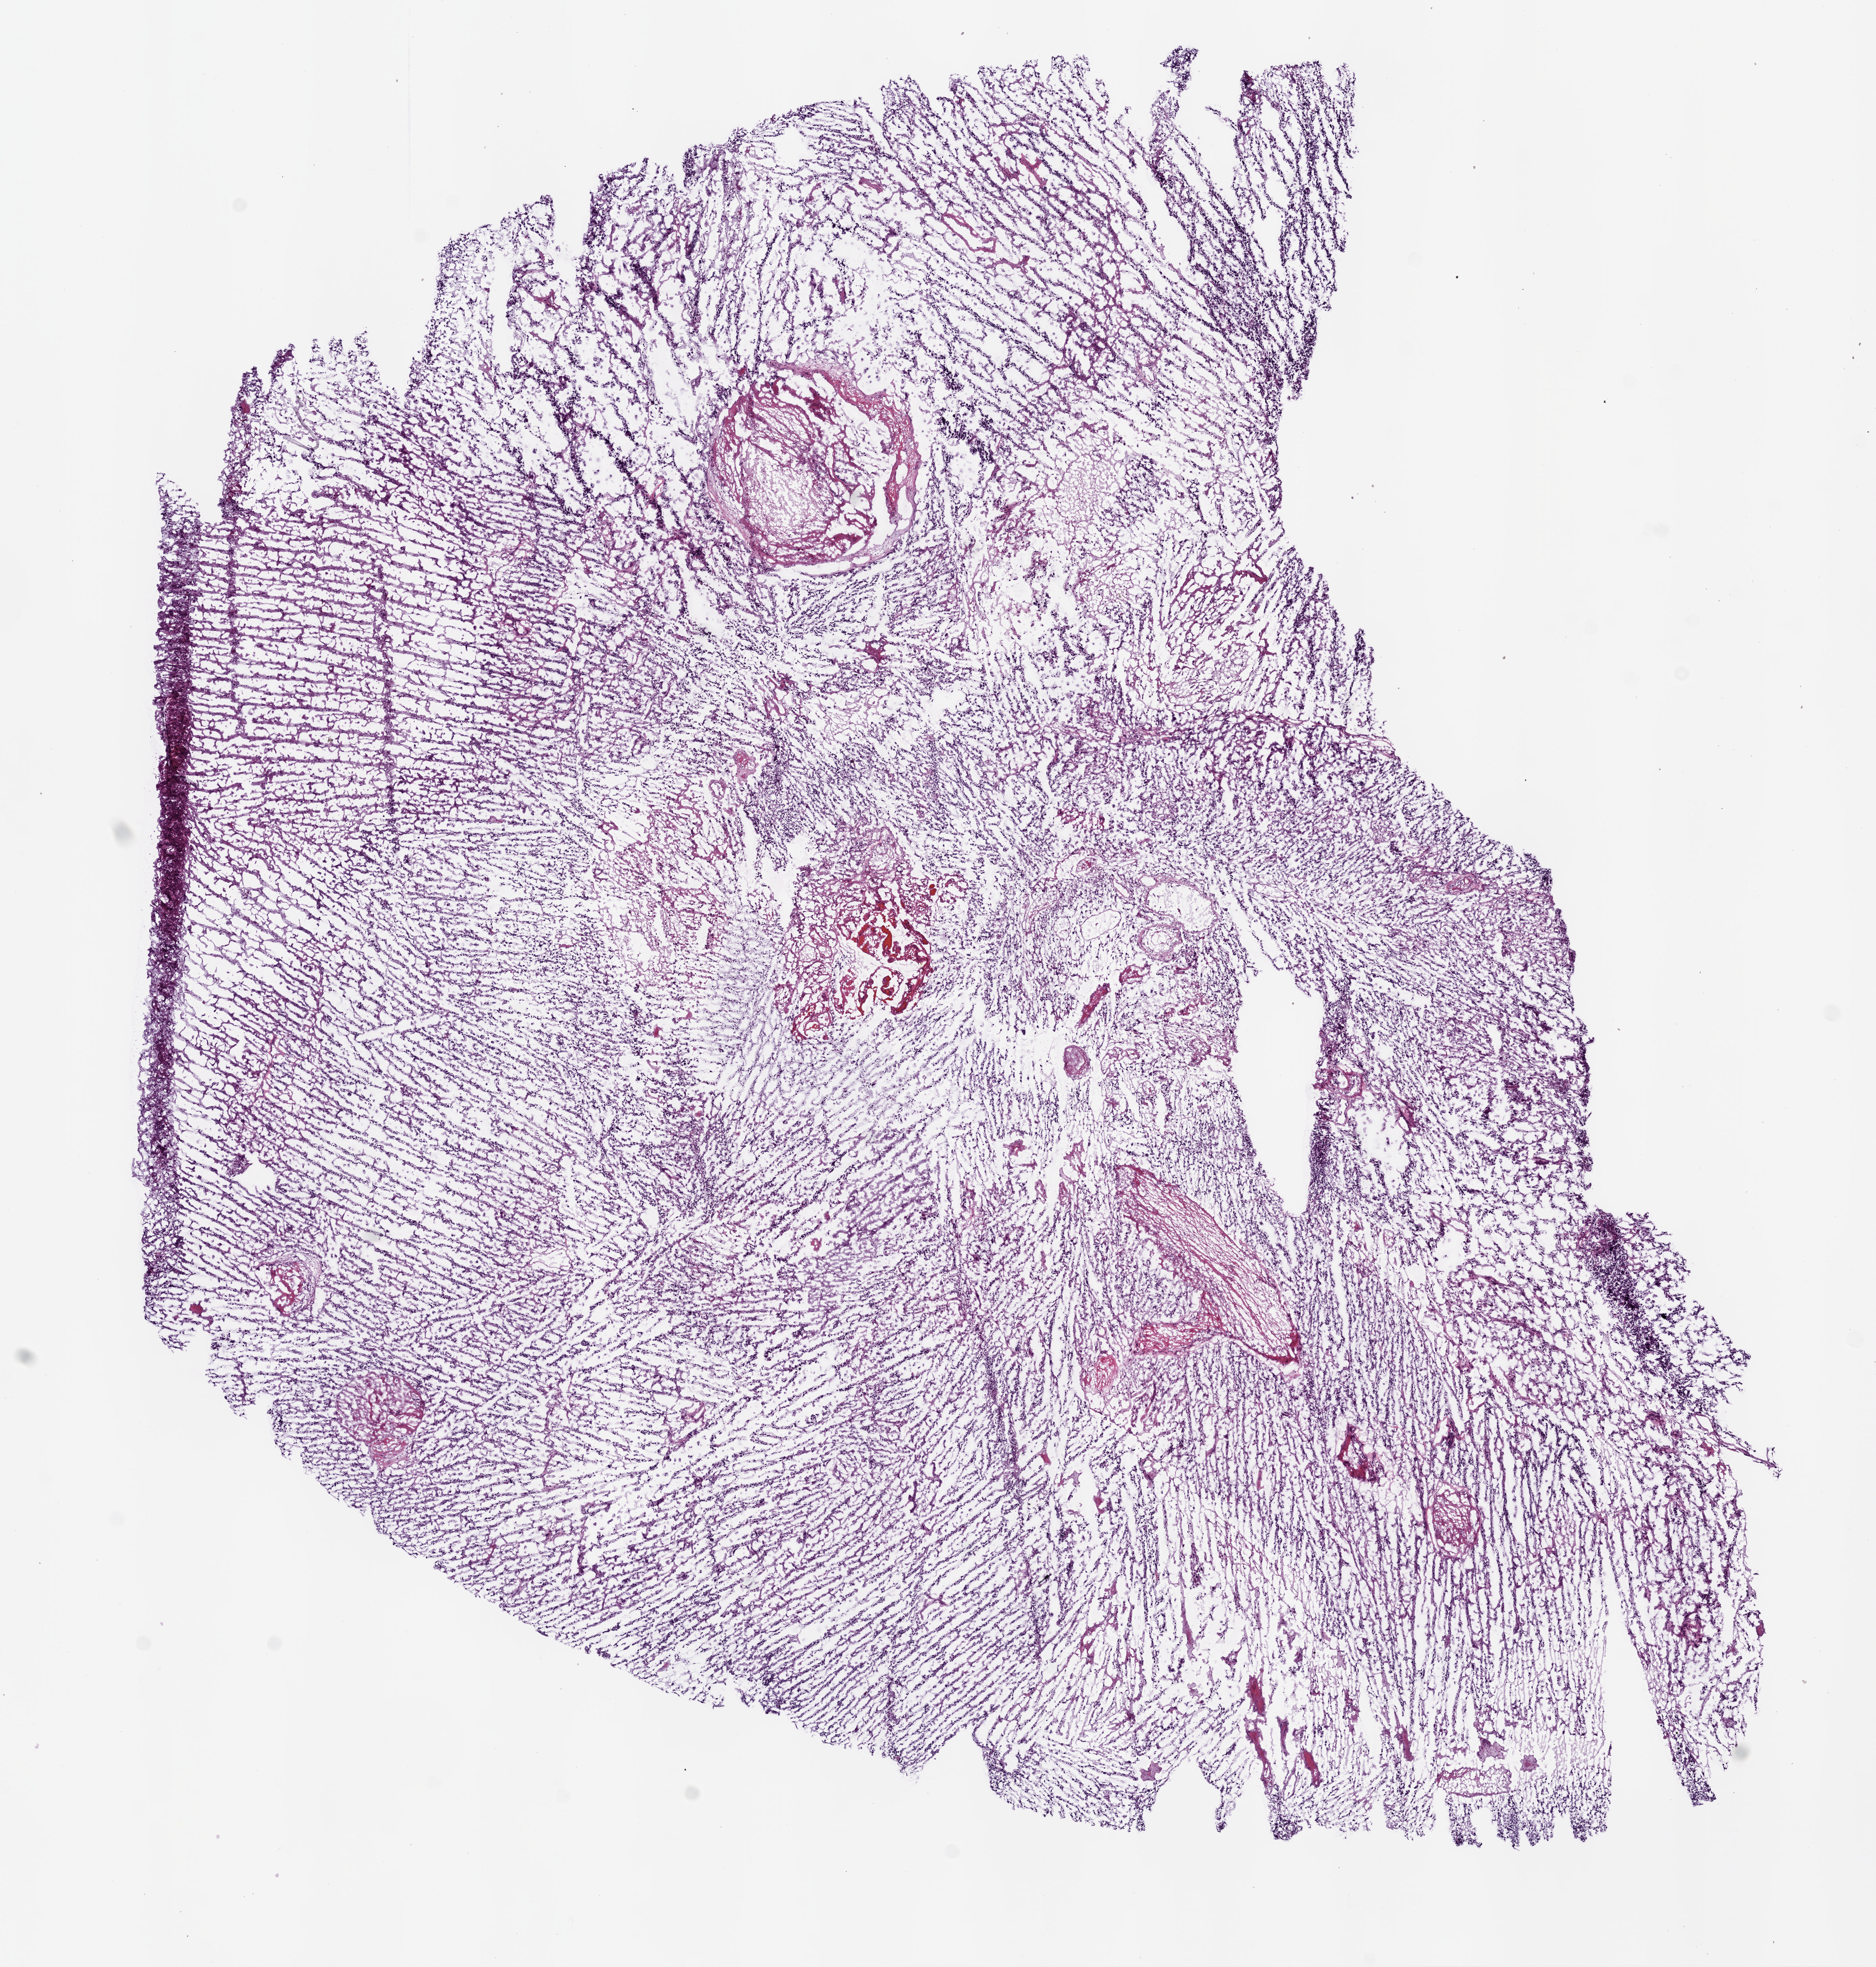
H&E whole-slide image, the whole scanned area (about 10.3 x 10.8 mm) at the scan's own resolution; frozen section; brain, primary tumour sample. Female patient; age at initial diagnosis 23 years. Composition of this section per pathologist review: tumour cells 100%, tumour nuclei 85%.
Histologic diagnosis: Glioblastoma.